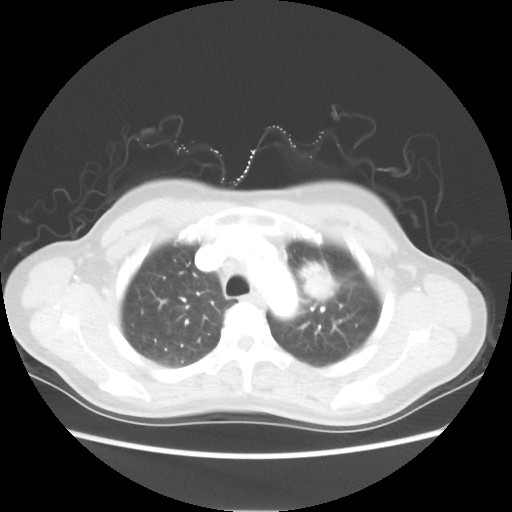
Chest CT, one axial slice; slice 42 of 54 in the series (ordered by position); reconstruction kernel STANDARD; 80 kVp; lung window (W 1500 / L -600 HU); 5 mm slice thickness; 512 × 512 image matrix. Female patient, age 53 years. Case-level facts recorded for this patient, not image findings: clinical TNM (as recorded): T1c N0 M0.
Structures marked on this image (bounding box drawn by a radiologist):
- lung tumour (recorded histology: adenocarcinoma): bounding box <295,258,348,308> (left, top, right, bottom; pixels)
- lung tumour (recorded histology: adenocarcinoma): <300,257,338,303>